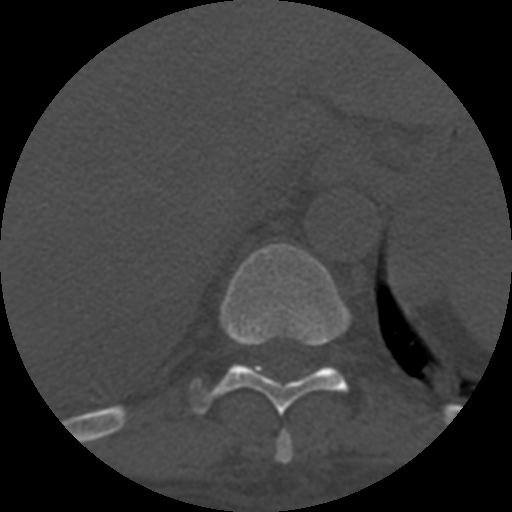
CT including the spine, one axial slice; slice 356 of 708 in the series (ordered by position); reconstruction kernel STANDARD; 120 kVp; one of 3 acquisitions stored at this slice position; bone window (W 1800 / L 400 HU); 1.25 mm slice thickness; 512 × 512 image matrix. Patient age 55 years. From the clinical record (not read from this slice): primary cancer: colon; vertebrae with lytic lesions (as recorded): T12, L1, L5.
Structures marked on this image (semi-automatic segmentation, software-assisted and operator-edited):
- T10 vertebra: box from (x=191, y=244) to (x=351, y=415) px
- T9 vertebra: (x=276, y=431)–(x=293, y=464)